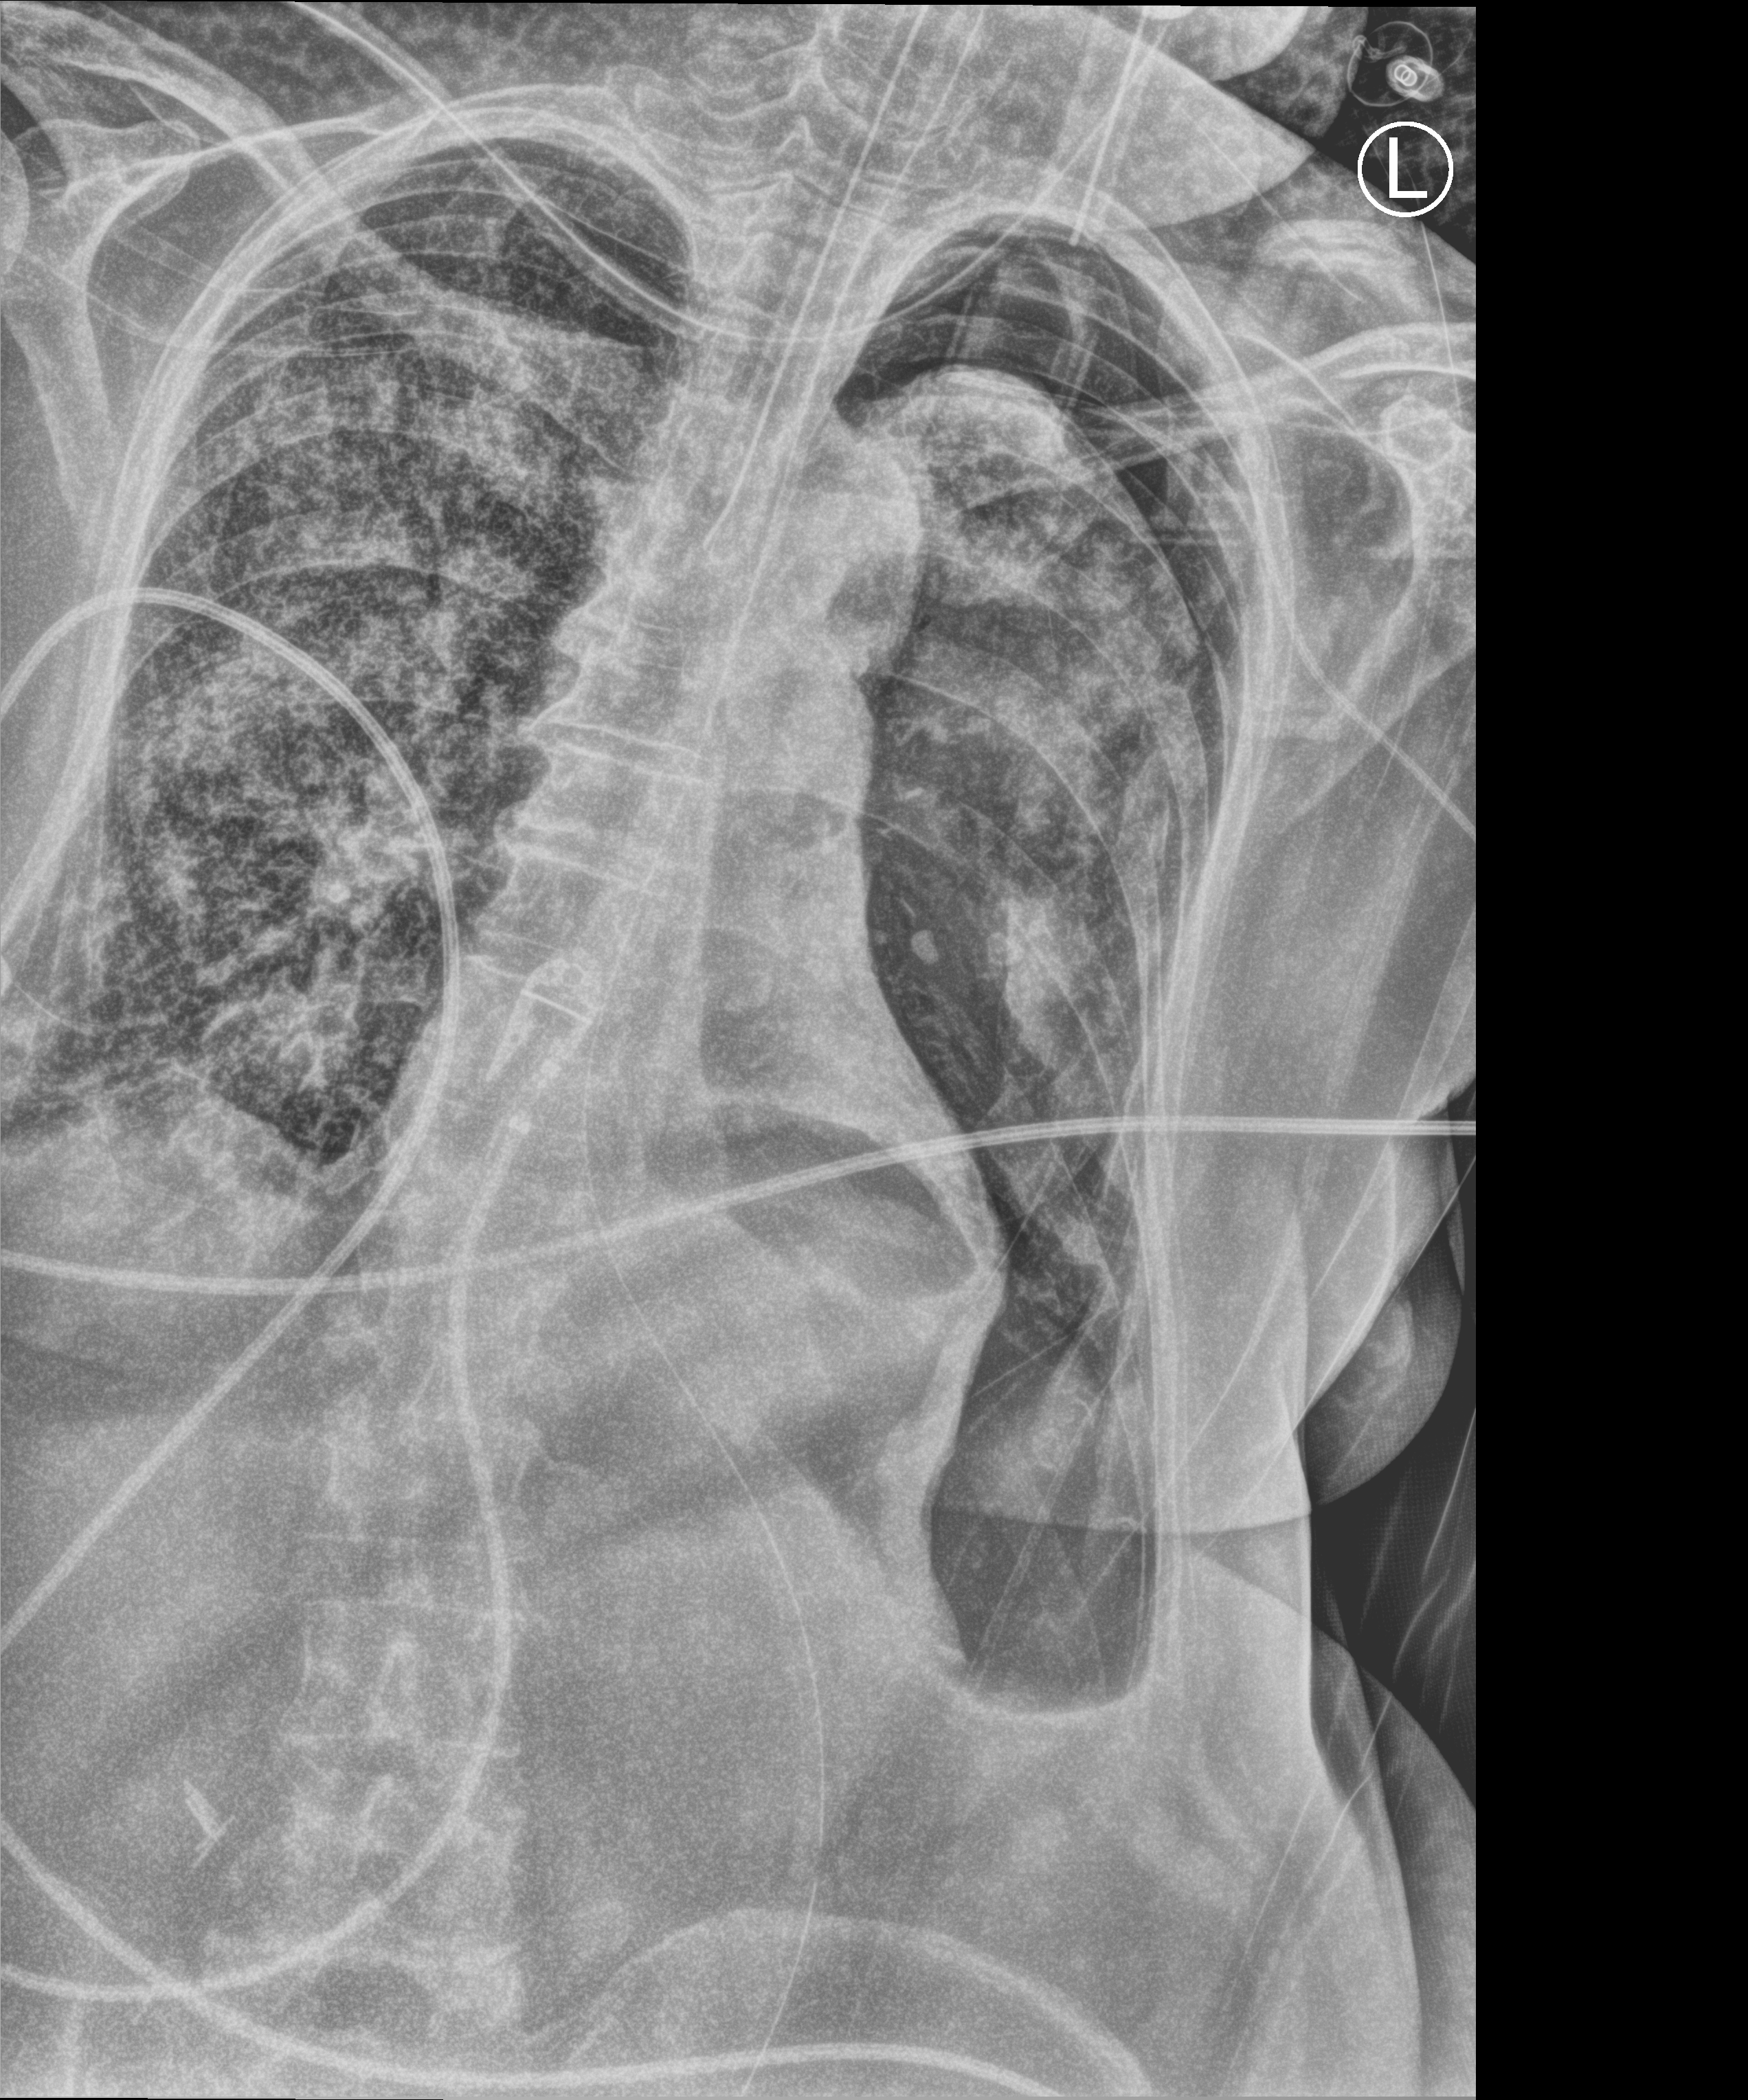
Bedside chest radiograph (computed radiography); anteroposterior (AP) projection. Female patient hospitalised with COVID-19, age 75–90 years.
Hospital-stay facts (about this admission, not read from this image; timing relative to this image not recorded):
- admitted to intensive care during this hospital stay: yes
- mechanically ventilated during this hospital stay: yes
- chronic kidney disease (admission record): no